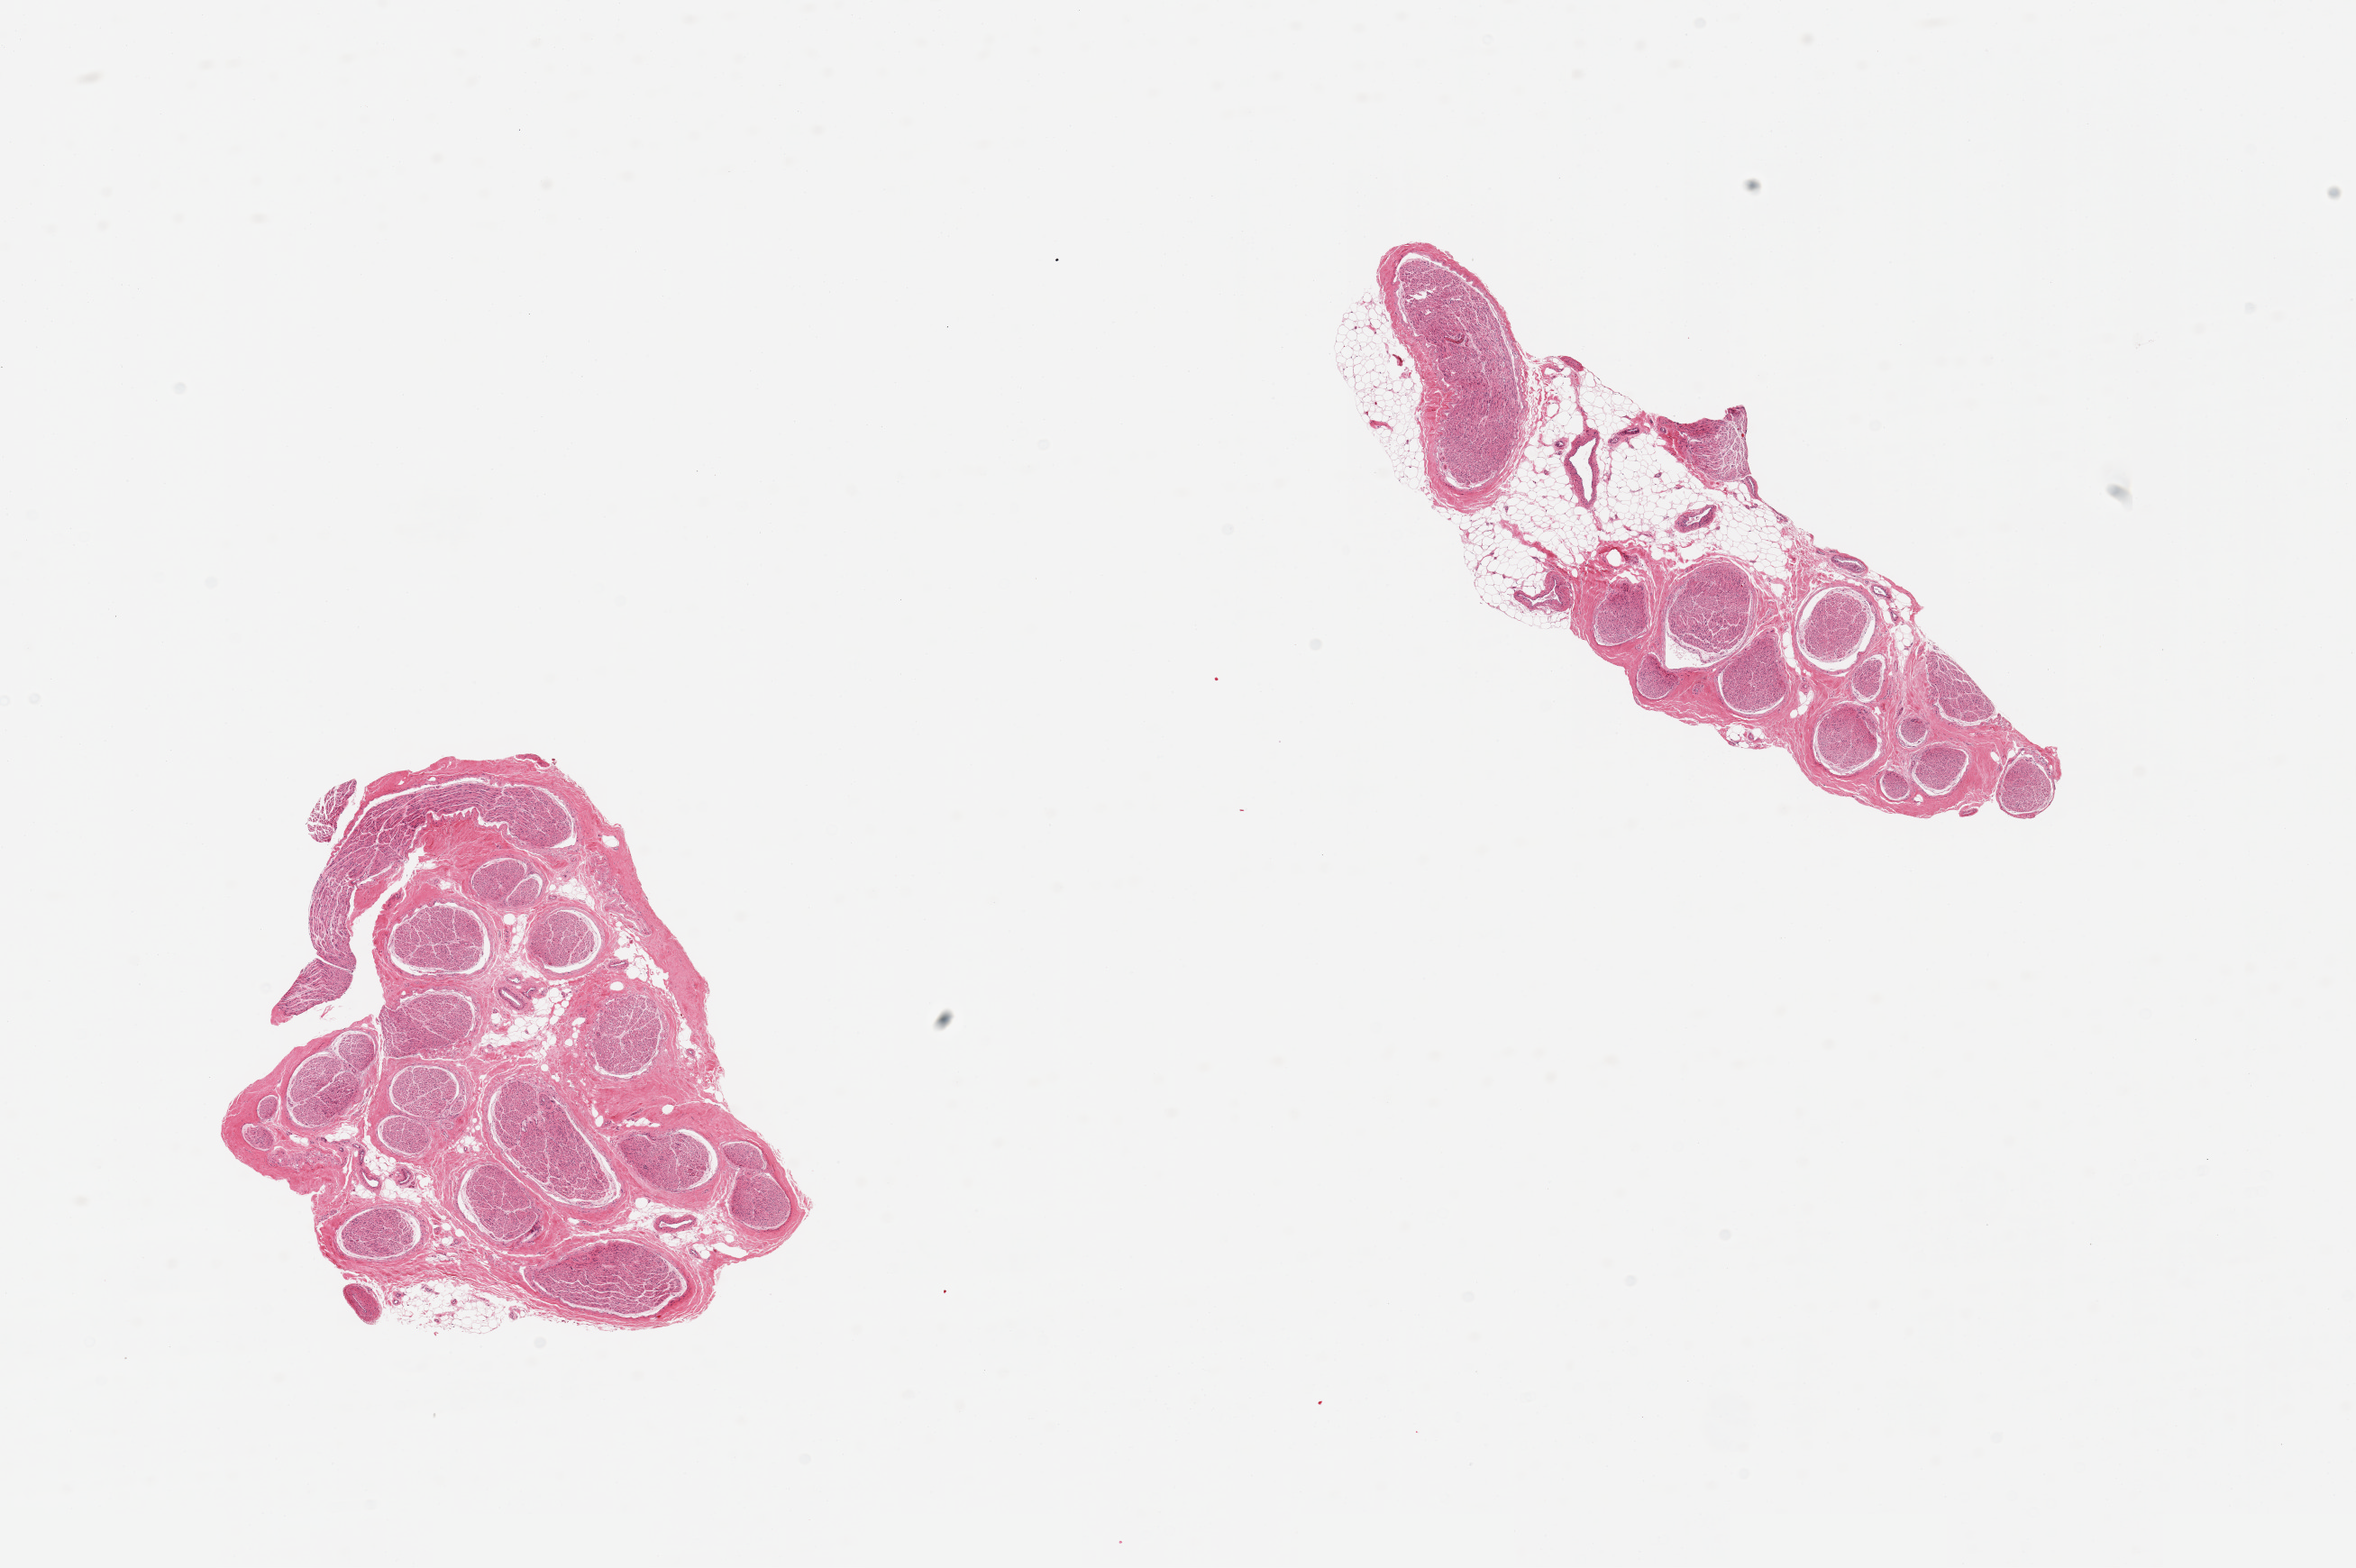
Hematoxylin and eosin (H&E) whole-slide image, brightfield — low-resolution overview of the scanned area, about 20.7 x 13.8 mm. PAXgene-fixed, paraffin-embedded tissue. Sampled site (target tissue): tibial nerve. Donor tissue sample. Donor sex: male.
Pathologist's review note for this sample: 2 pieces; 5% to 20% internal fat.